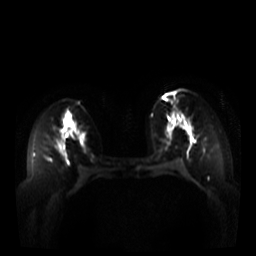
Breast MRI, one axial slice; position 20 of 44 along the scan axis; diffusion-weighted series; image 2 of 4 stored at this slice position (different b-values; order by instance number); 3 T; 256 × 256 image matrix, field of view 340 × 340 mm. Female patient.
Annotated regions visible in this slice (outlined manually by an expert reader):
- tumour on diffusion-weighted imaging: box from (x=184, y=122) to (x=188, y=128) px